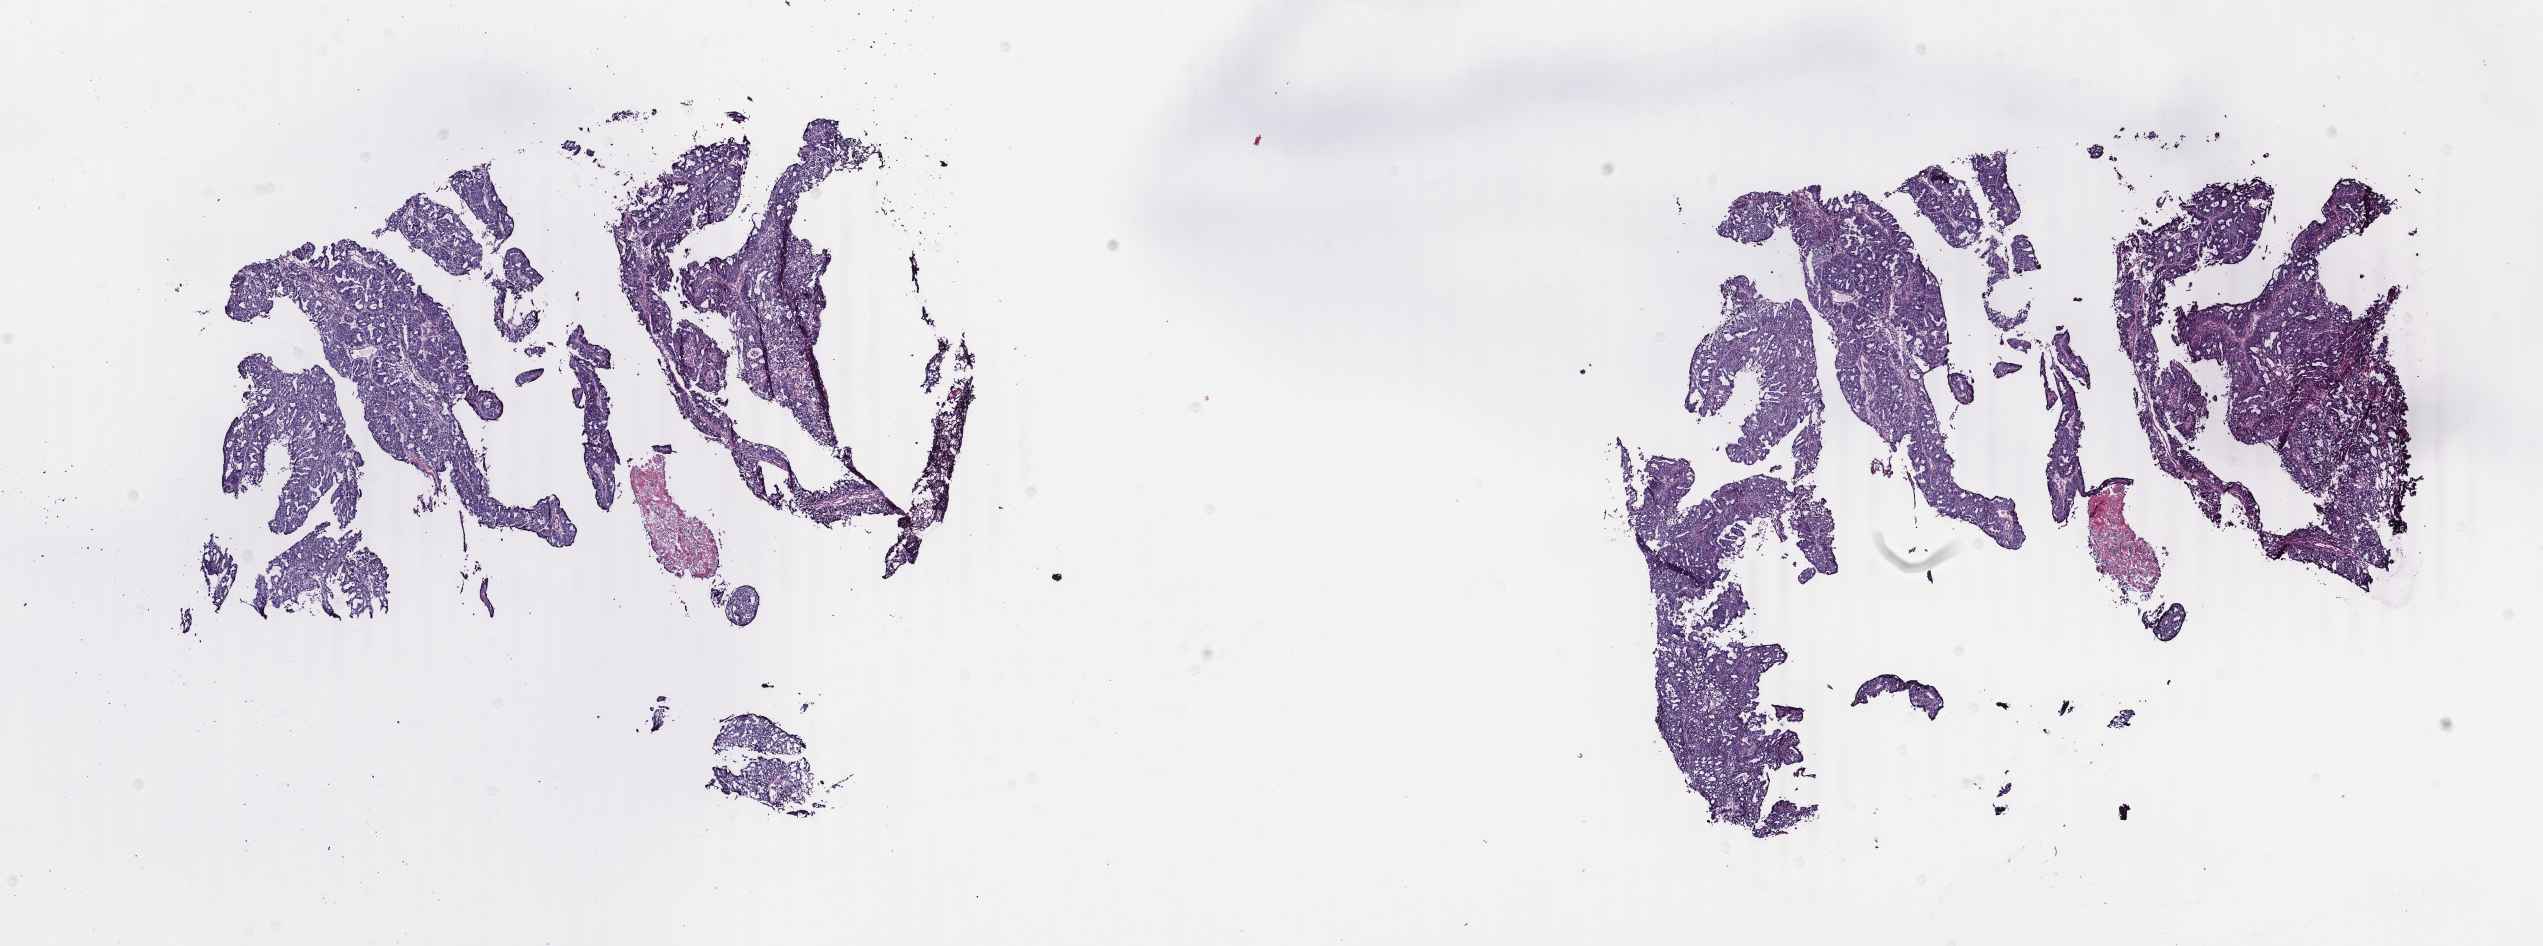
H&E whole-slide image — whole scanned area (about 20.2 x 7.5 mm) shown as a low-resolution overview; frozen section; sample: primary tumour, uterus. Female, age 62 years at initial diagnosis. Histologic grade: G3 (poorly differentiated). Composition of this section per pathologist review: tumour cells 95%, tumour nuclei 90%, normal cells 0%, stromal cells 0%, necrosis 5%. Infiltration values recorded for this section: lymphocyte infiltration 0%, monocyte infiltration 0%, neutrophil infiltration 0%.
Histologic diagnosis: Endometrioid adenocarcinoma, NOS. FIGO stage: IA.